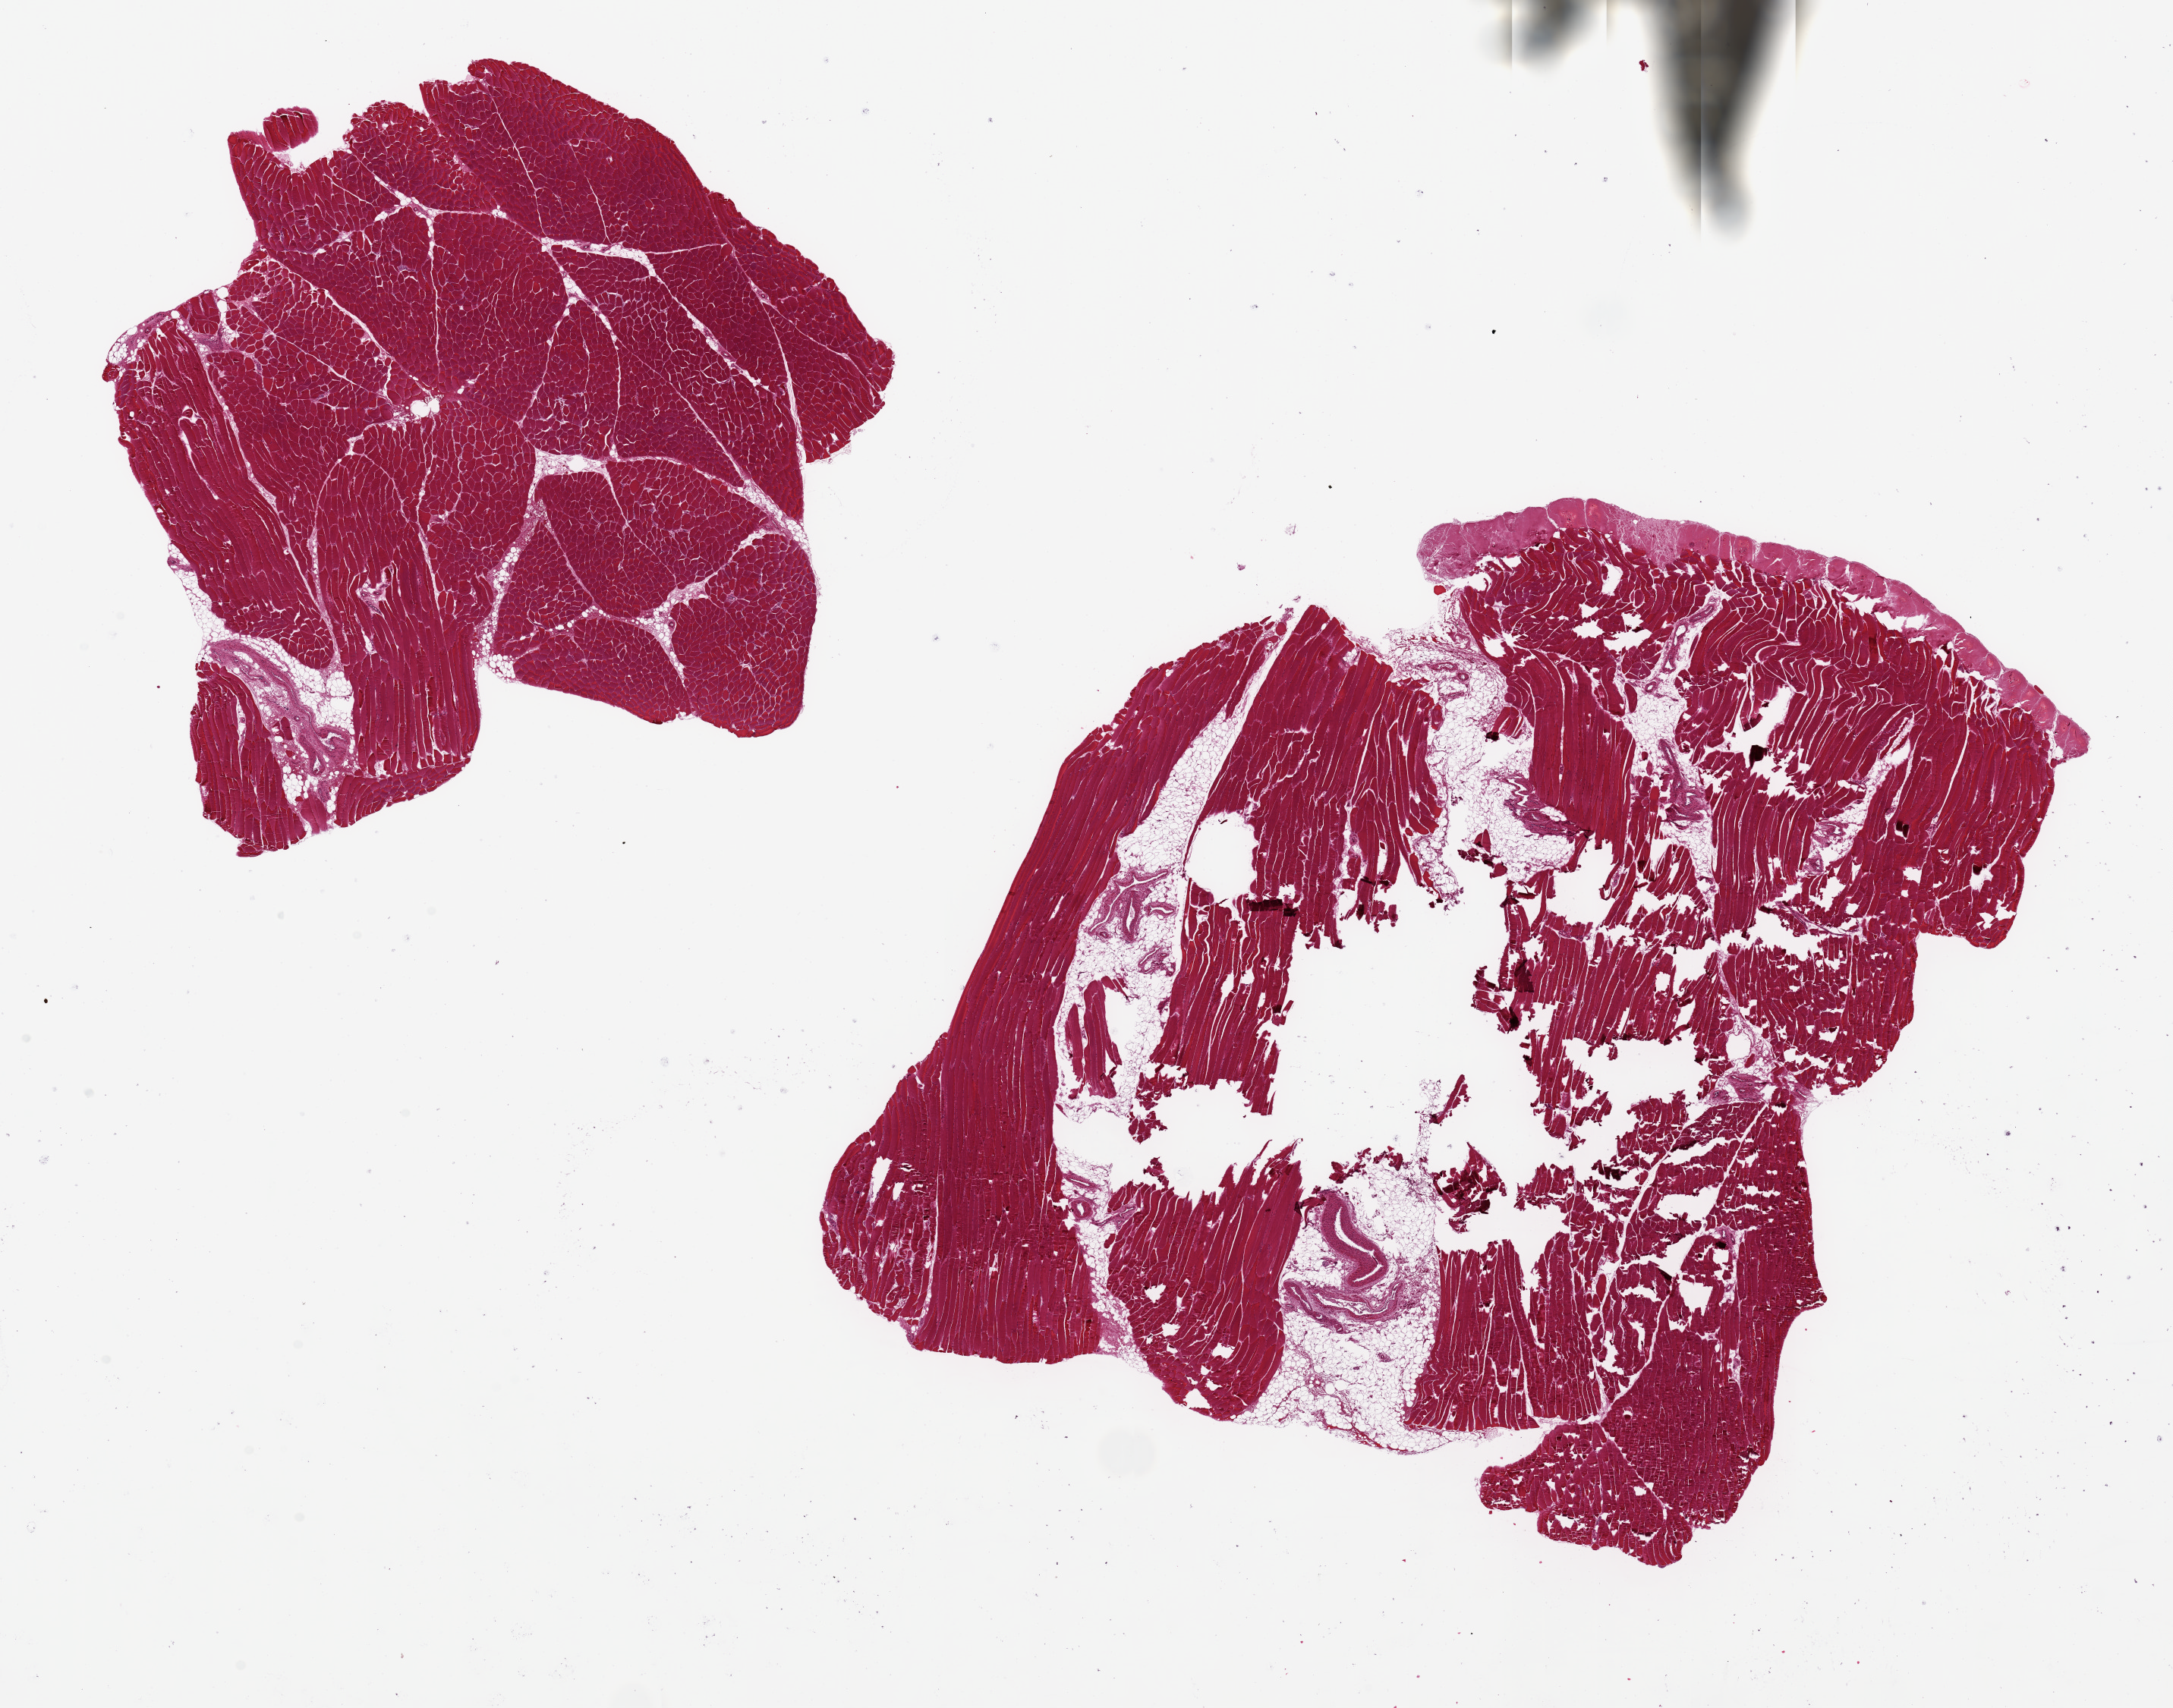
Whole-slide image, hematoxylin and eosin (H&E) stain, shown as a low-resolution overview of the whole scanned area (about 22.6 x 17.8 mm), PAXgene-fixed, paraffin-embedded tissue, section of skeletal muscle (target tissue), tissue donor sample. Donor sex: female.
Review note (as recorded): 2 pieces, ~8x8 & 10x10mm, larger piece has extensive fracture artifact, probable fixation effect.